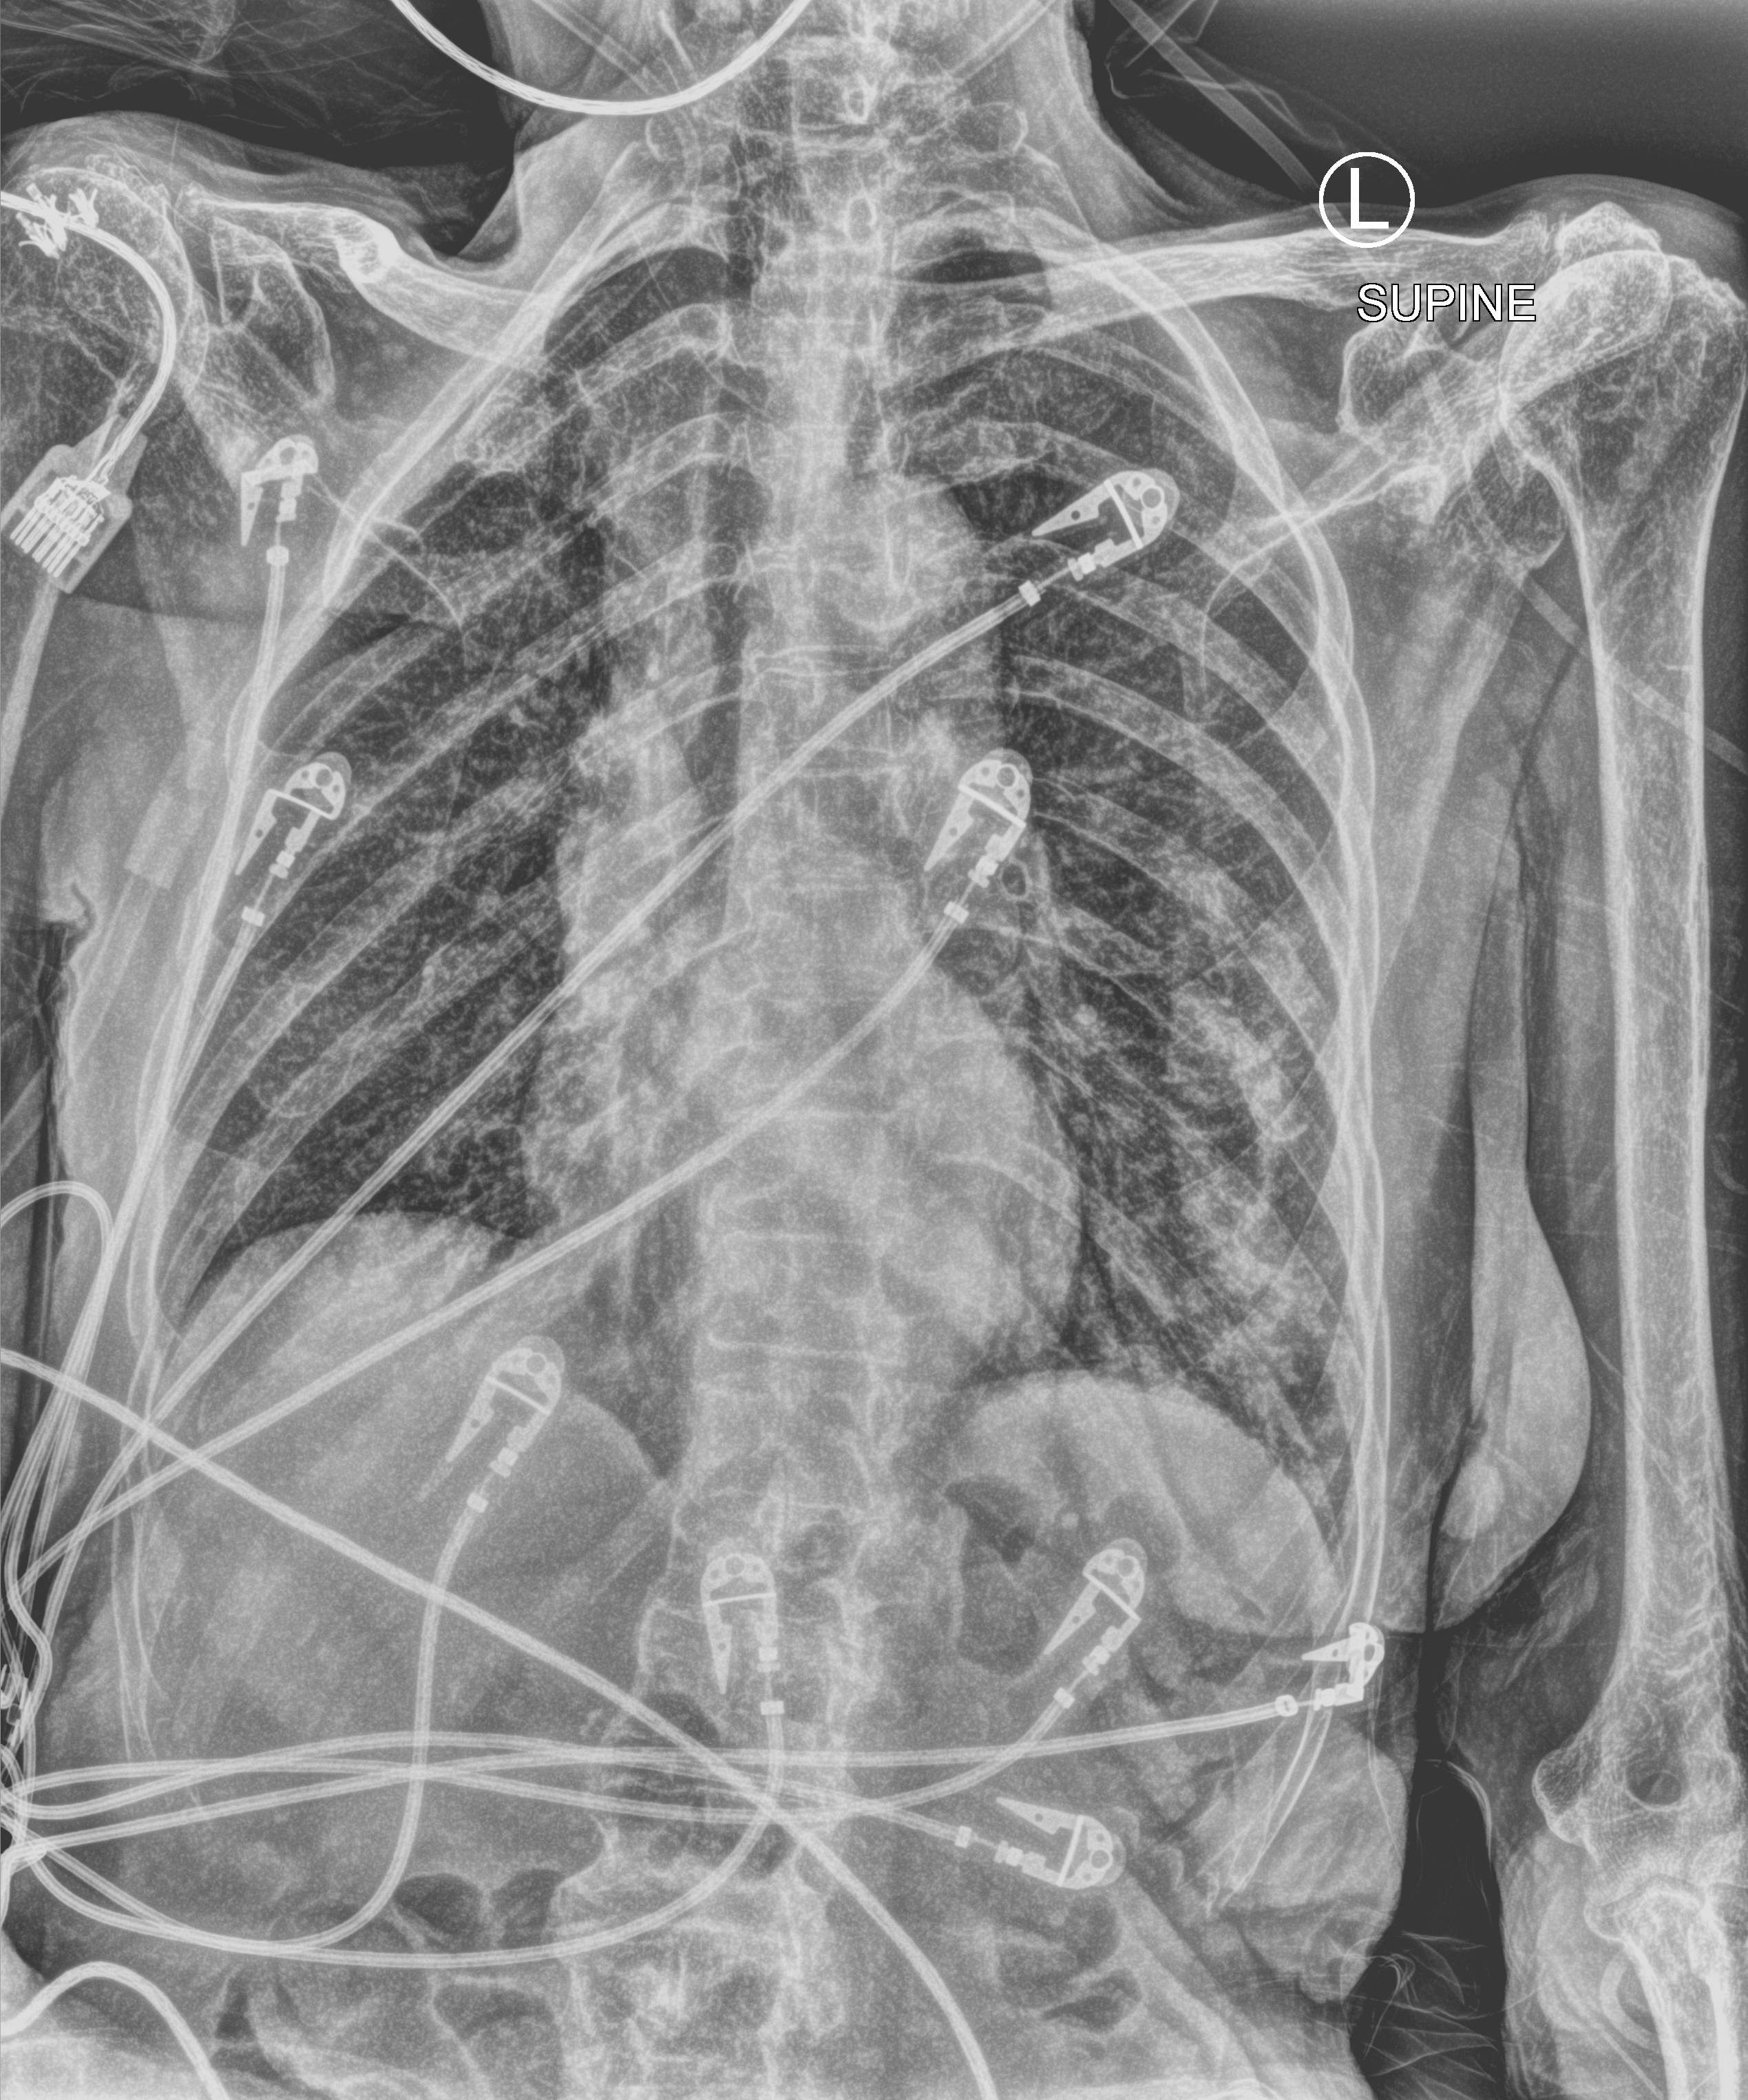
Portable chest radiograph; anteroposterior (AP) projection. Female patient hospitalised with COVID-19, age 75–90 years.
From the hospital-stay record, not from the radiograph (when in the stay this image was taken is not recorded):
- admitted to intensive care during this hospital stay: yes